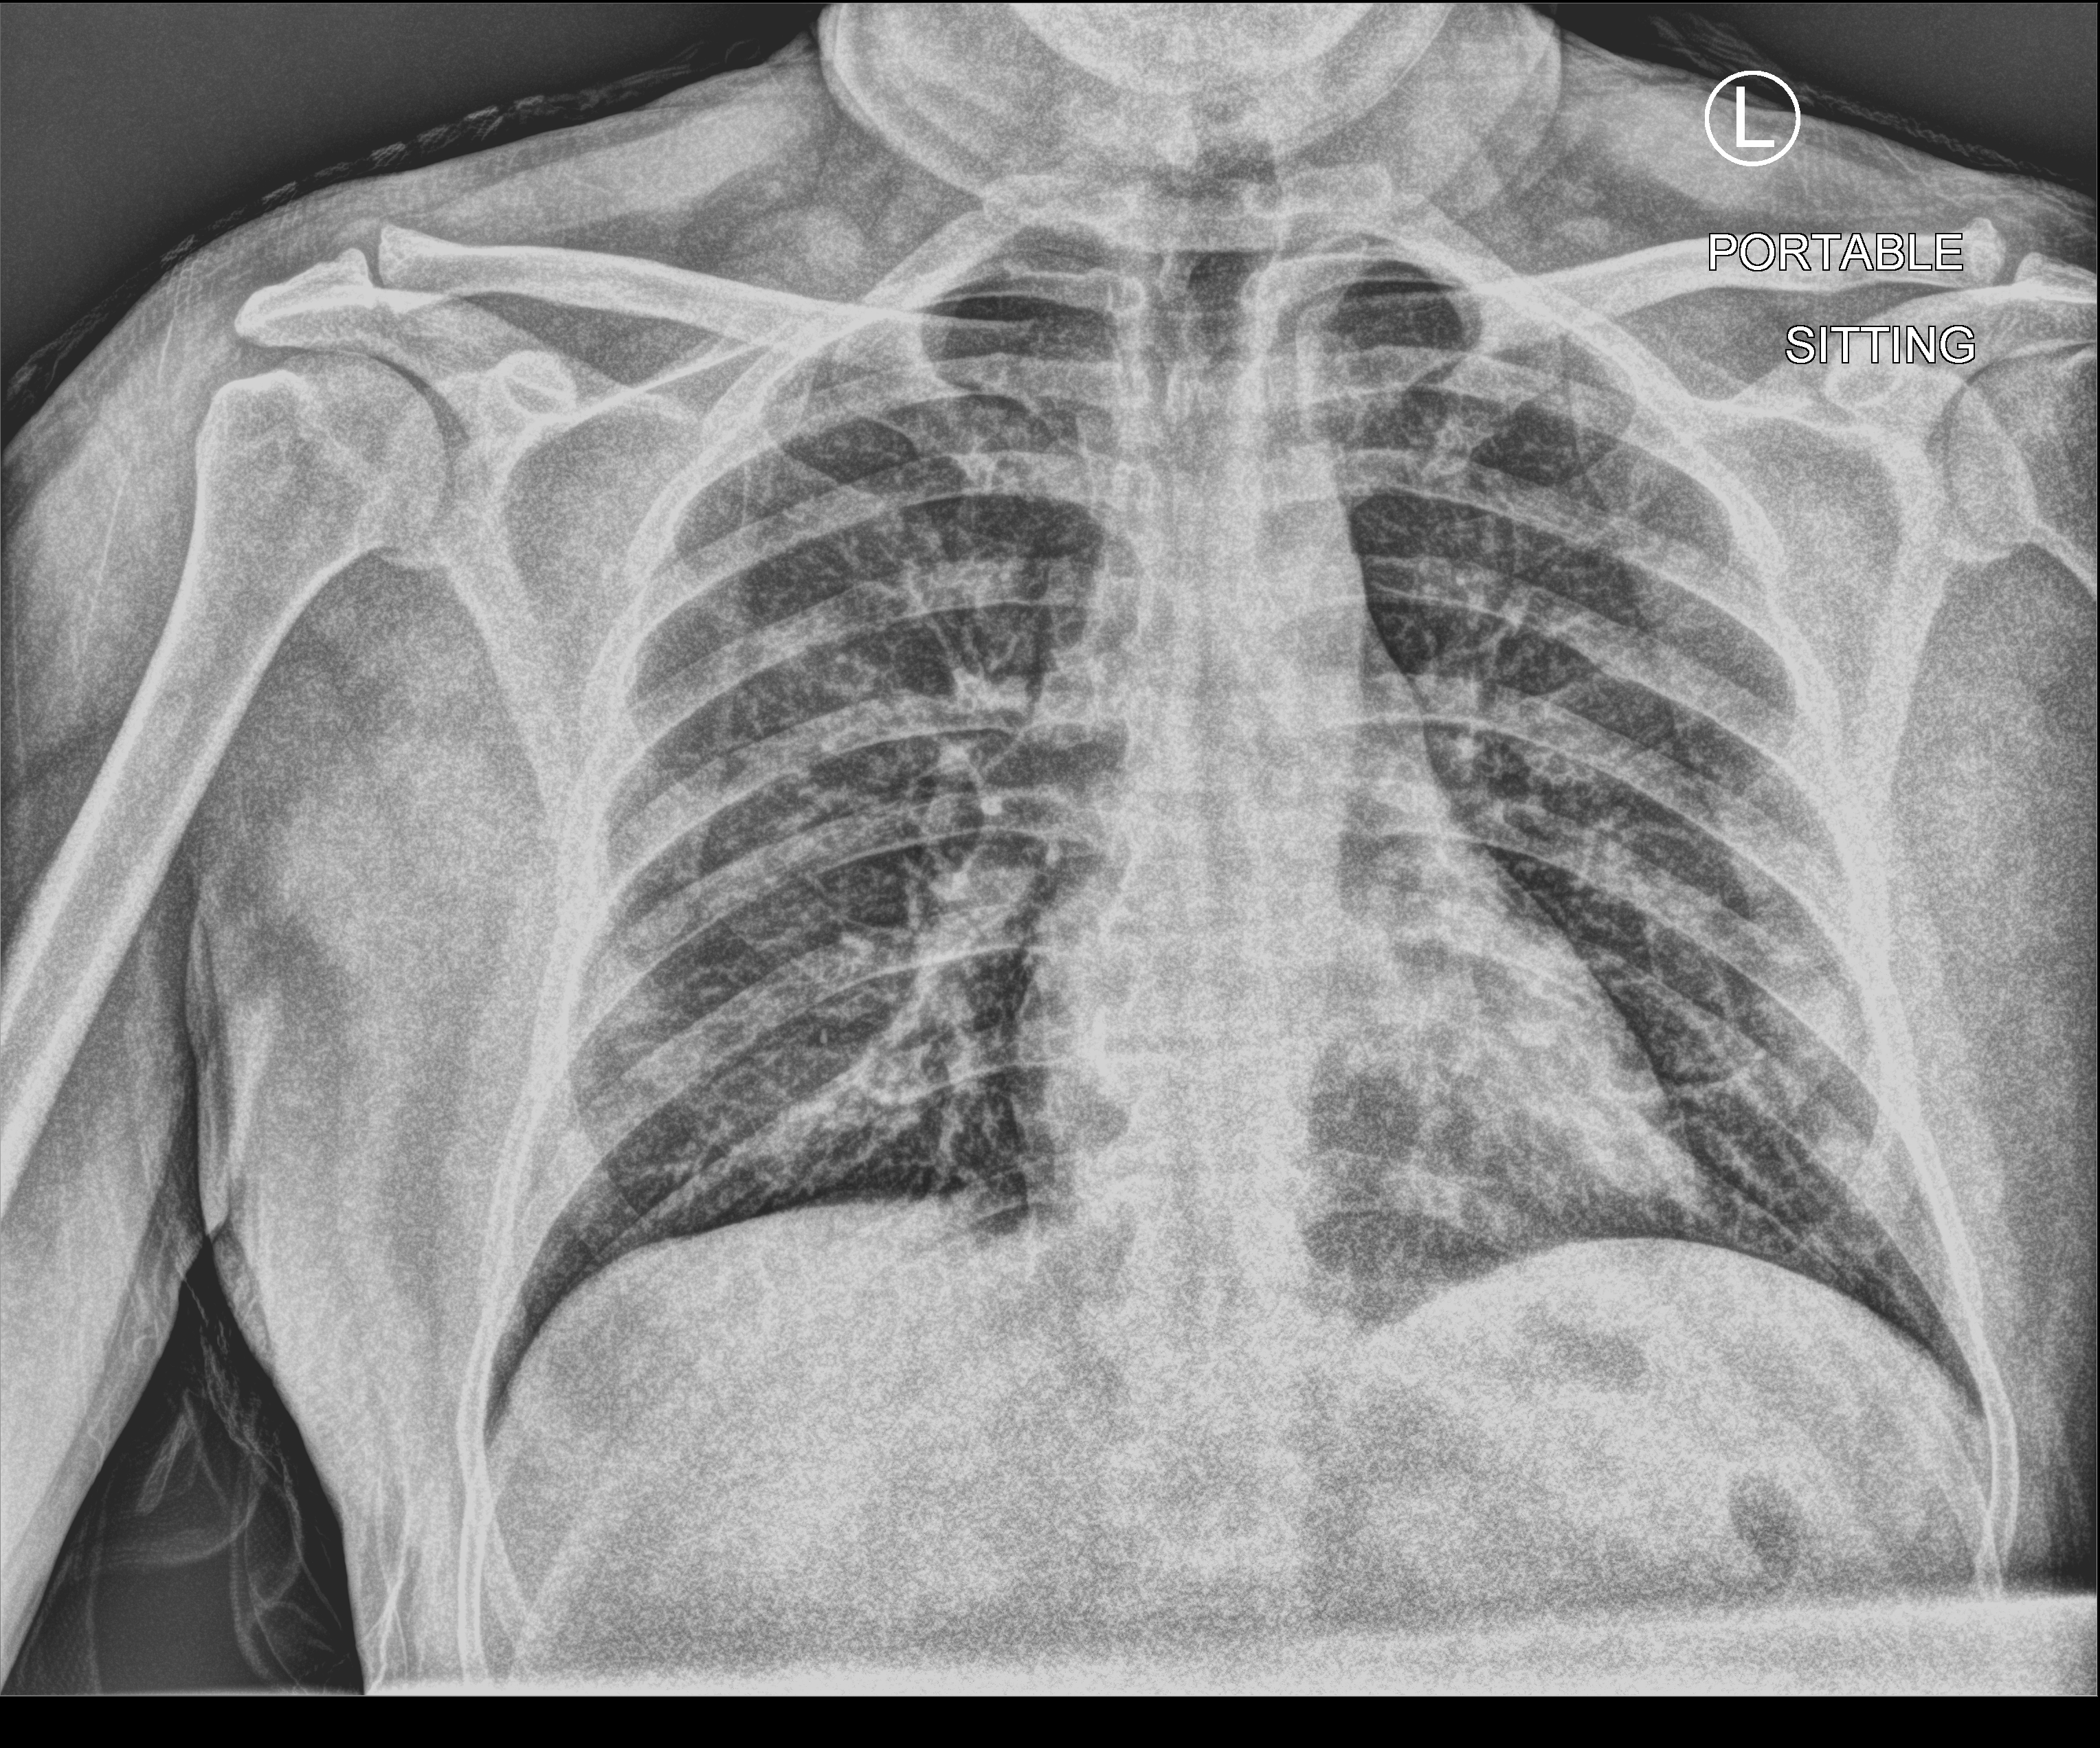
Bedside chest radiograph (computed radiography); anteroposterior (AP) projection. Patient hospitalised with COVID-19; male, aged 18–59 years.
From the hospital-stay record, not from the radiograph (when in the stay this image was taken is not recorded): COPD (admission record): no; admitted to intensive care during this hospital stay: no; diabetes (admission record): no.